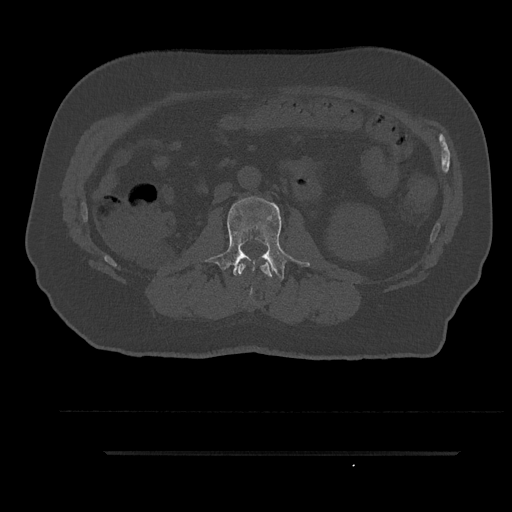
CT including the spine, one axial slice; 120 kVp; bone window (W 1800 / L 400 HU); 0.5 mm slice thickness; 512 × 512 image matrix, field of view 432 × 432 mm. Male patient, age 63 years. Case-level facts recorded for this patient, not image findings: primary cancer: renal.
Annotated regions visible in this slice (semi-automatically segmented with operator editing):
- L1 vertebra: box from (x=237, y=261) to (x=273, y=278) px
- L2 vertebra: (x=204, y=197)–(x=309, y=292)